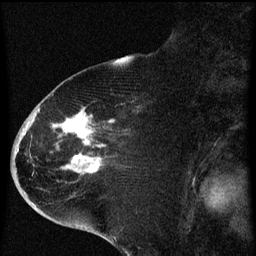
Breast MRI (dynamic contrast-enhanced), one sagittal slice; slice 29 of 60 in the series (ordered by position); dynamic contrast-enhanced series, image 2 of 4 at this slice position (ordered by acquisition); 1.5 T; TE 4.2 ms, TR 8 ms; 2 mm slice thickness; 256 × 256 image matrix, field of view 180 × 180 mm. Female patient, age 71 years.
Annotated regions visible in this slice (semi-automatically segmented with operator editing):
- analysis volume of interest (the breast-tissue region the enhancement analysis was run in; not a lesion): bounding box <32,86,140,205> (left, top, right, bottom; pixels)
- tumour enhancement mask (voxels above the 70 % enhancement threshold inside the analysis volume of interest): <38,110,114,175>